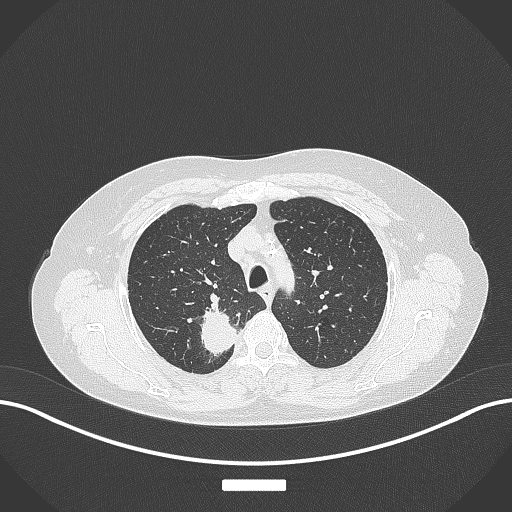
Chest CT, one axial slice; position 299 of 357 along the scan axis; reconstruction kernel B70f; 120 kVp; lung window (W 1500 / L -600 HU); 512 × 512 image matrix, field of view 400 × 400 mm. Female patient, age 62 years. From the clinical record (not read from this slice): clinical TNM (as recorded): T1c N1 M0.
Annotated regions visible in this slice (bounding box drawn by a radiologist):
- lung tumour (recorded histology: squamous cell carcinoma): box from (x=191, y=300) to (x=240, y=358) px